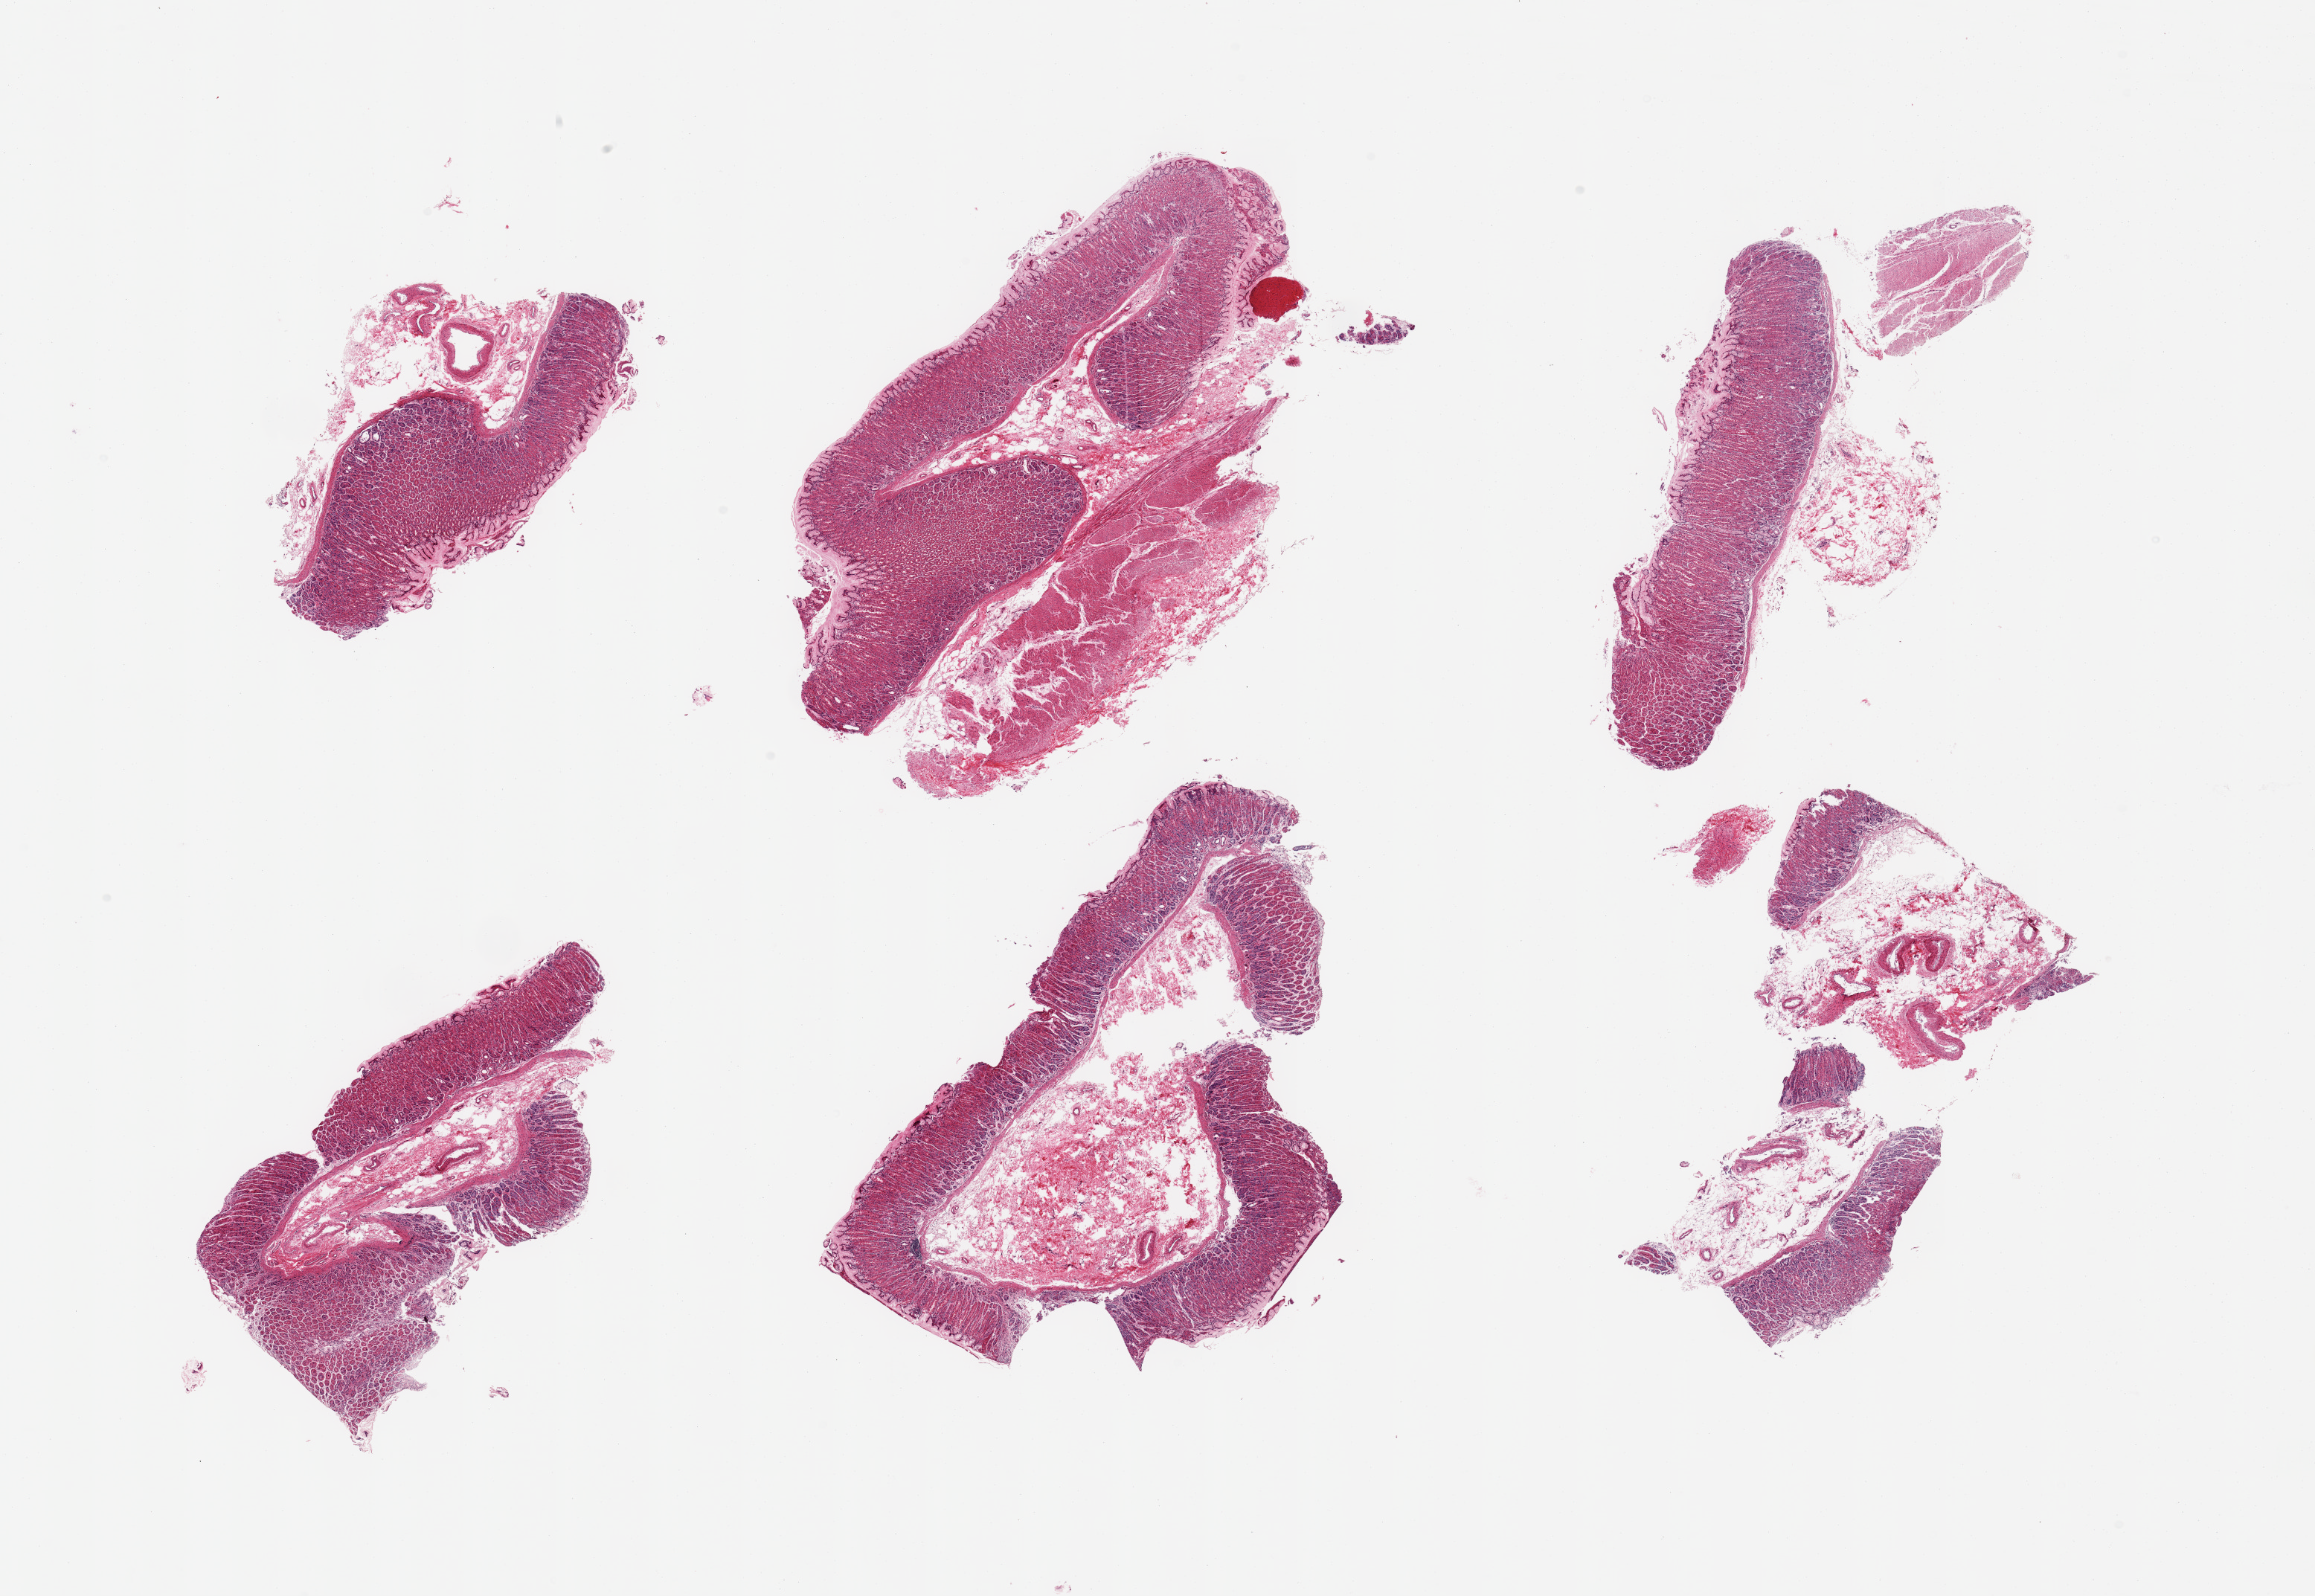
Digitized H&E-stained section — a low-resolution overview of the entire scanned area, about 24.6 x 17.0 mm. PAXgene-fixed paraffin-embedded (PFPE) section. Section of stomach (target tissue). Donor tissue sample. Donor sex: male.
Pathologist's review note for this sample: 6 pieces, abundant well-preserved mucosa up to ~1mm, 50-100% of thickness.